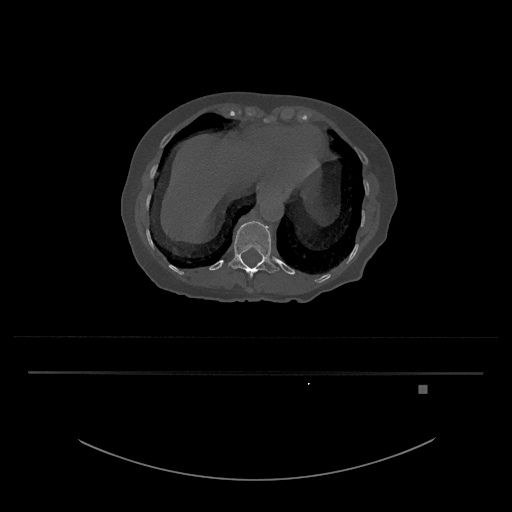
CT including the spine, one axial slice. Position 615 of 797 along the scan axis. Reconstruction kernel Br40s/3. 120 kVp. Bone window (W 1800 / L 400 HU). 0.5 mm slice thickness. 512 × 512 image matrix. Female patient, age 57 years. Case-level facts recorded for this patient, not image findings: primary cancer: cervical.
Structures marked on this image (semi-automatically segmented with operator editing):
- T12 vertebra: box from (x=228, y=221) to (x=279, y=277) px